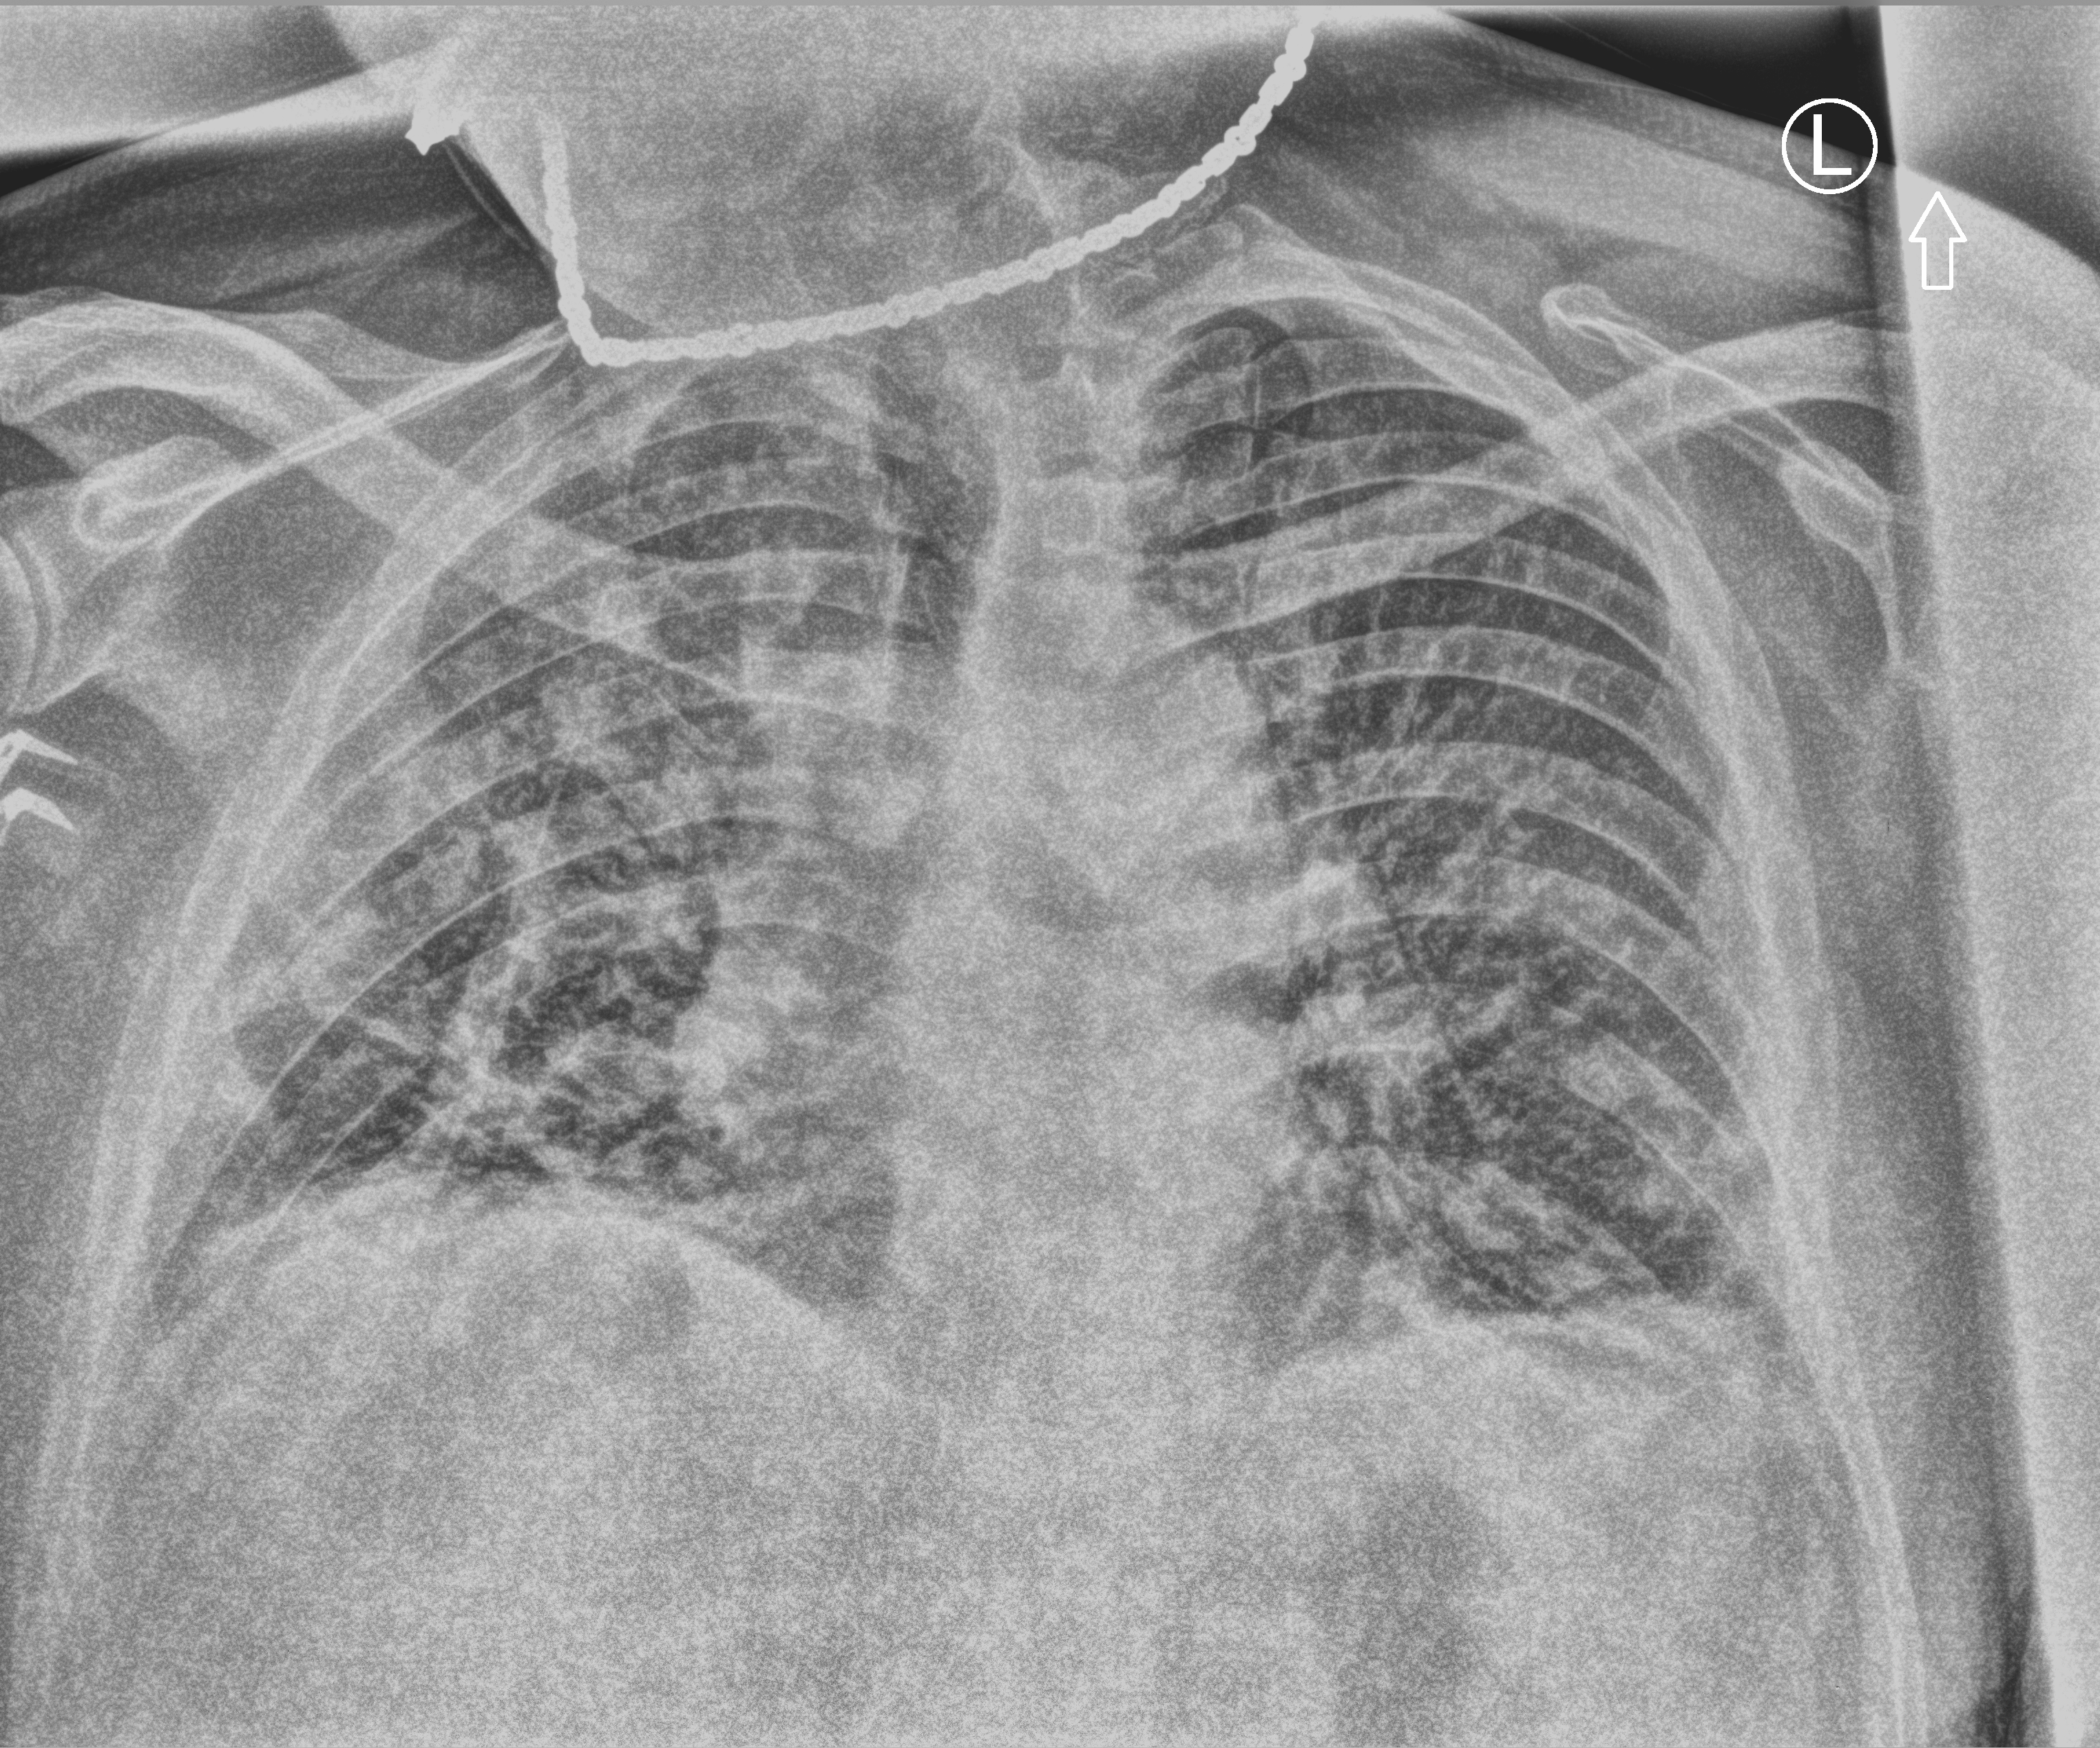
Chest X-ray (portable). Patient hospitalised with COVID-19; male, aged 18–59 years.
Hospital-stay facts (about this admission, not read from this image; timing relative to this image not recorded): length of hospital stay: 8 days; admitted to intensive care during this hospital stay: no; mechanically ventilated during this hospital stay: no.